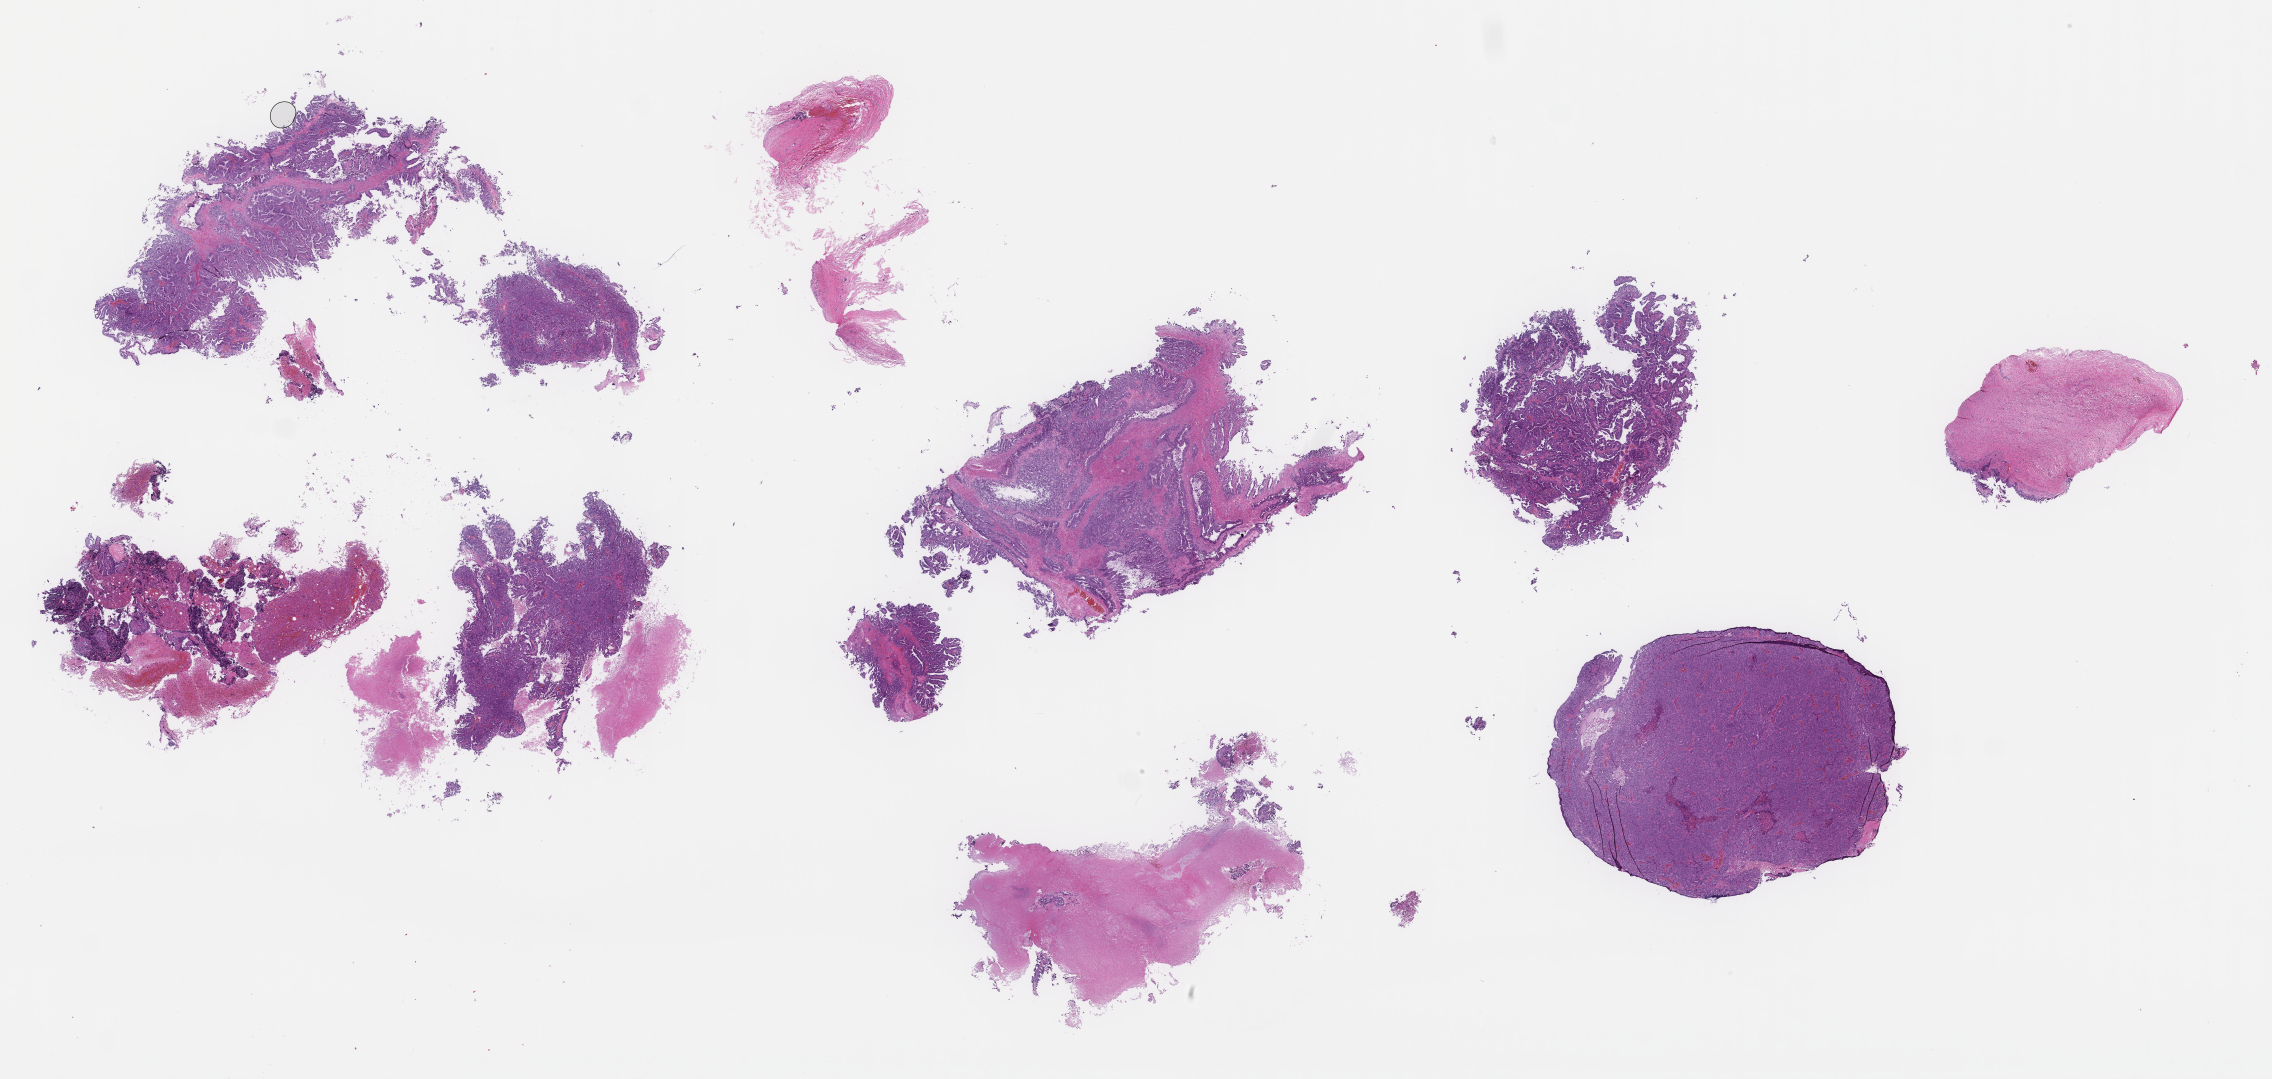
Whole-slide image, H&E stain — whole scanned area (about 36.7 x 17.4 mm) shown as a low-resolution overview. Formalin-fixed, paraffin-embedded (FFPE) tissue. Tissue site: ovary. Collected at baseline (before treatment). Female patient.
• this section: primary tumor
• diagnosis: Ovarian Carcinoma